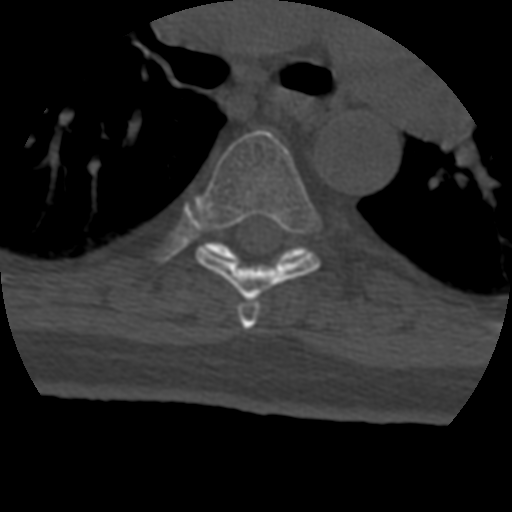
CT including the spine, one axial slice. Reconstruction kernel STANDARD. 120 kVp. Bone window (W 1800 / L 400 HU). 1.25 mm slice thickness. 512 × 512 image matrix. Patient age 69 years. Case-level facts recorded for this patient, not image findings: primary cancer: prostate.
Outlined on this slice (semi-automatically segmented with operator editing):
- T5 vertebra: bounding box <238,299,260,329> (left, top, right, bottom; pixels)
- T6 vertebra: <196,130,321,300>
- T7 vertebra: <204,241,310,262>